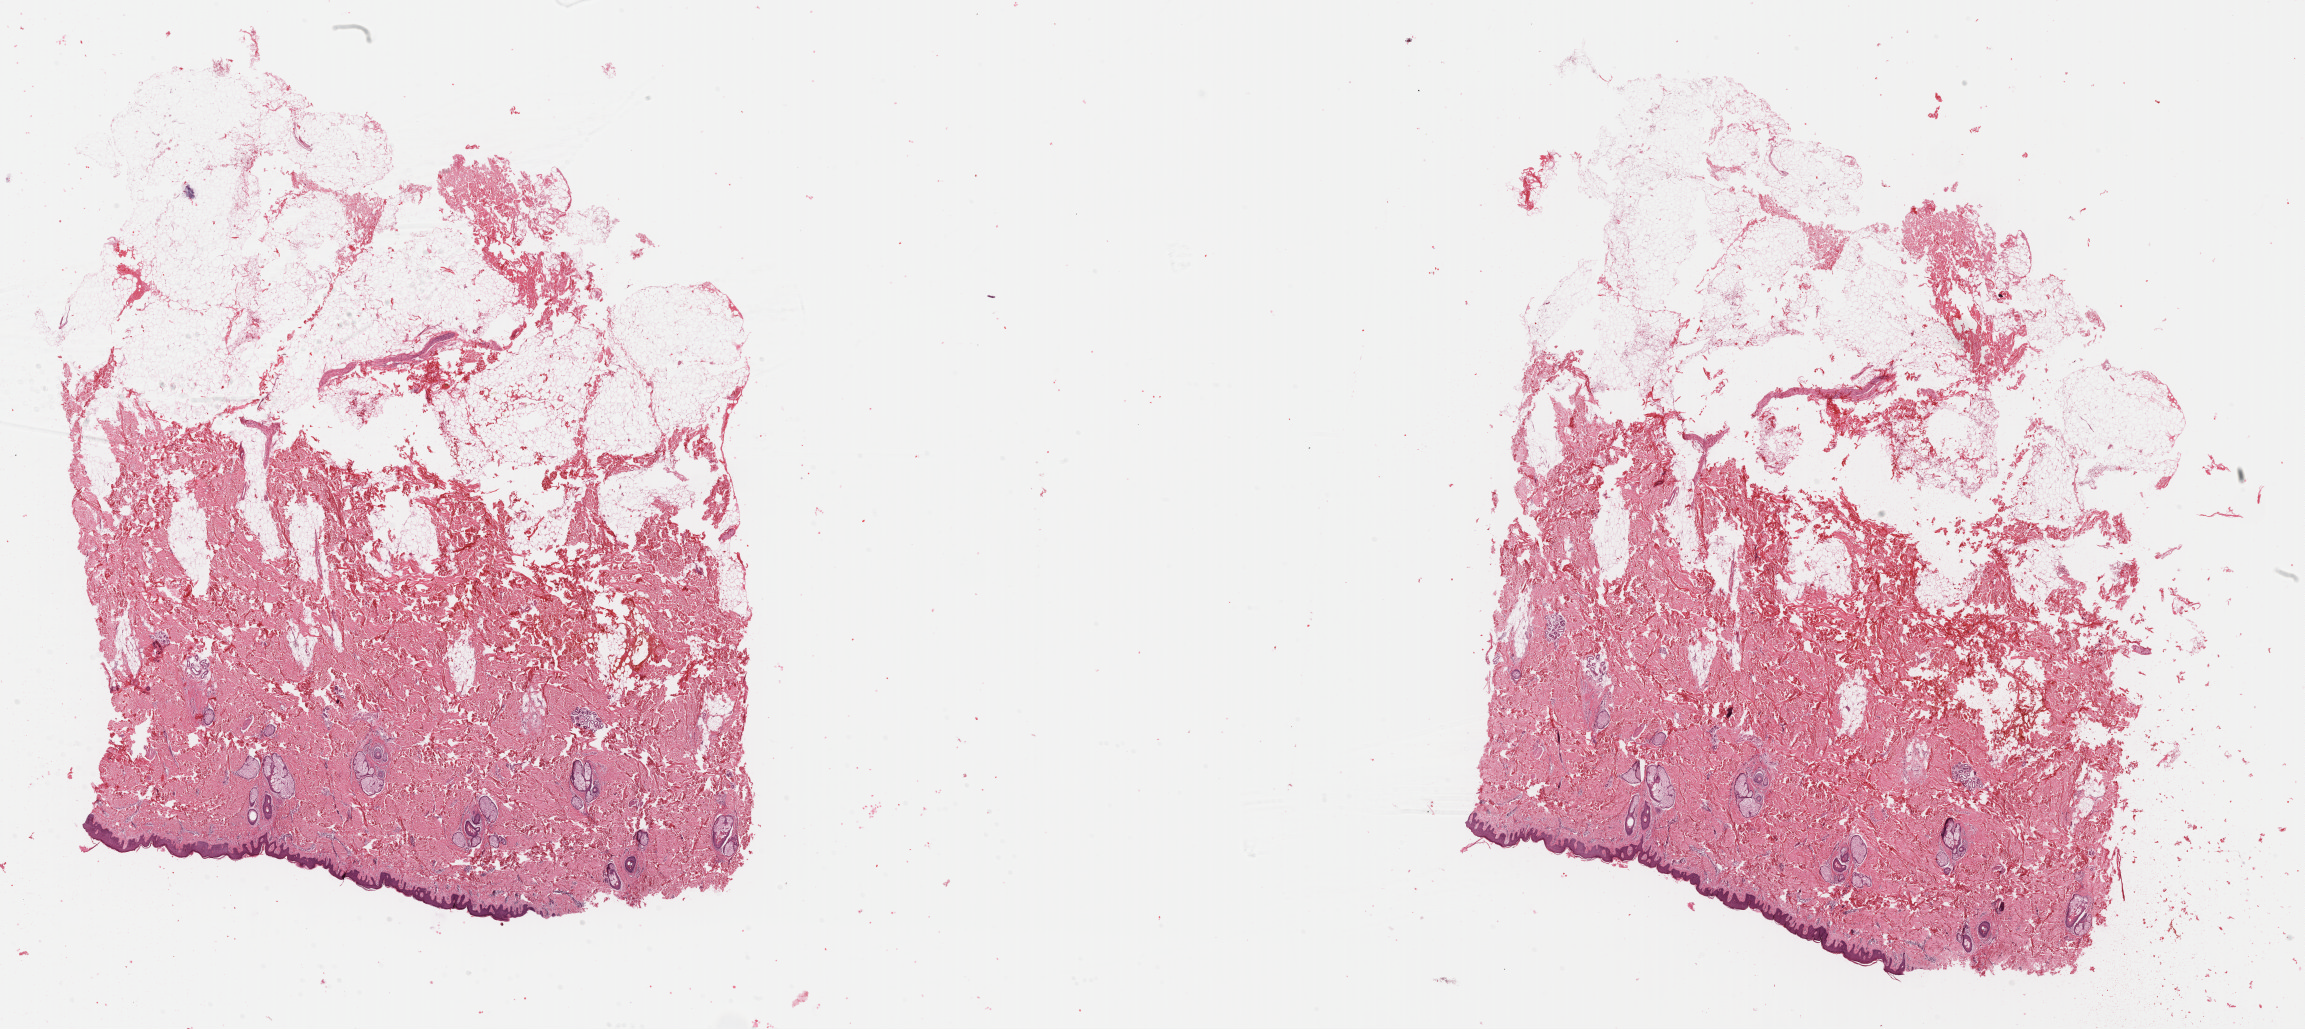
Hematoxylin and eosin (H&E) stained whole-slide image — low-resolution overview of the scanned area, about 36.2 x 16.2 mm (acquisition: 40x scan), formalin-fixed paraffin-embedded (FFPE) diagnostic section, sample: primary tumour, skin. Male, age 43 years at initial diagnosis.
* pathologic diagnosis: Malignant melanoma, NOS
* AJCC pathologic stage: IIIA